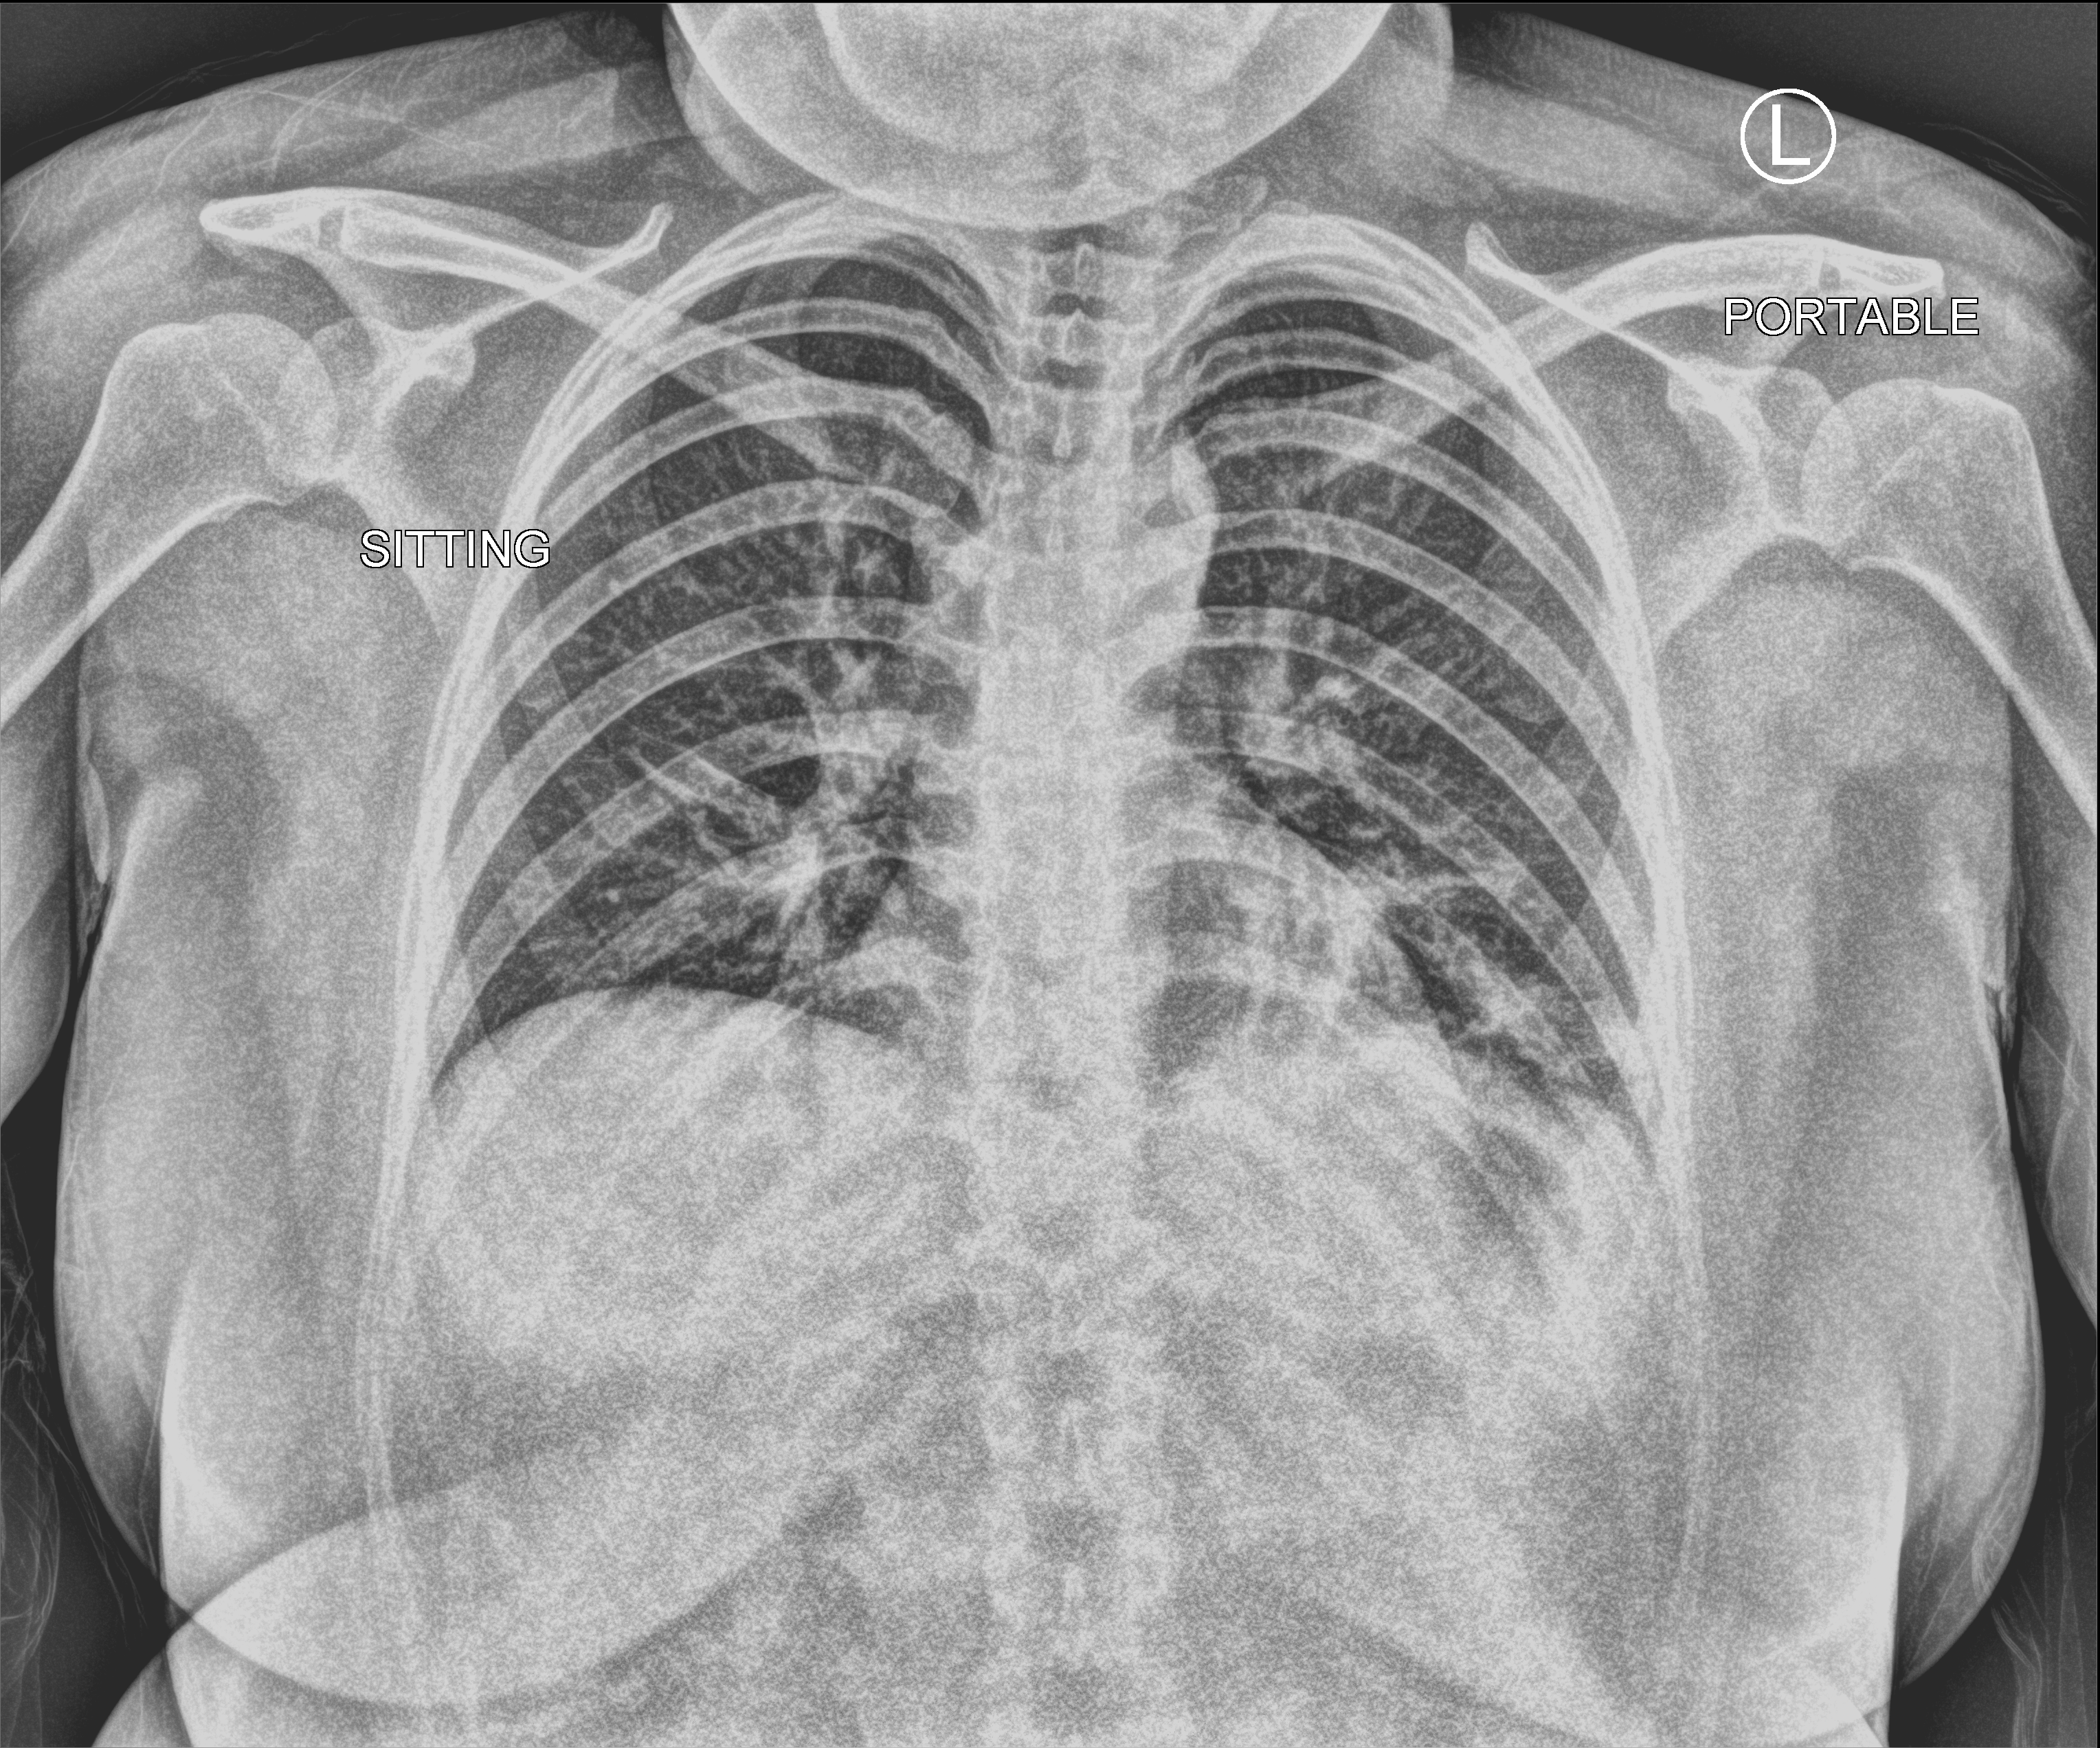
Chest X-ray (portable). Female patient hospitalised with COVID-19, age 18–59 years.
Admission-level facts for this patient (not findings on this image; timing relative to this image not recorded): admitted to intensive care during this hospital stay: no; mechanically ventilated during this hospital stay: no; length of hospital stay: 1 day.